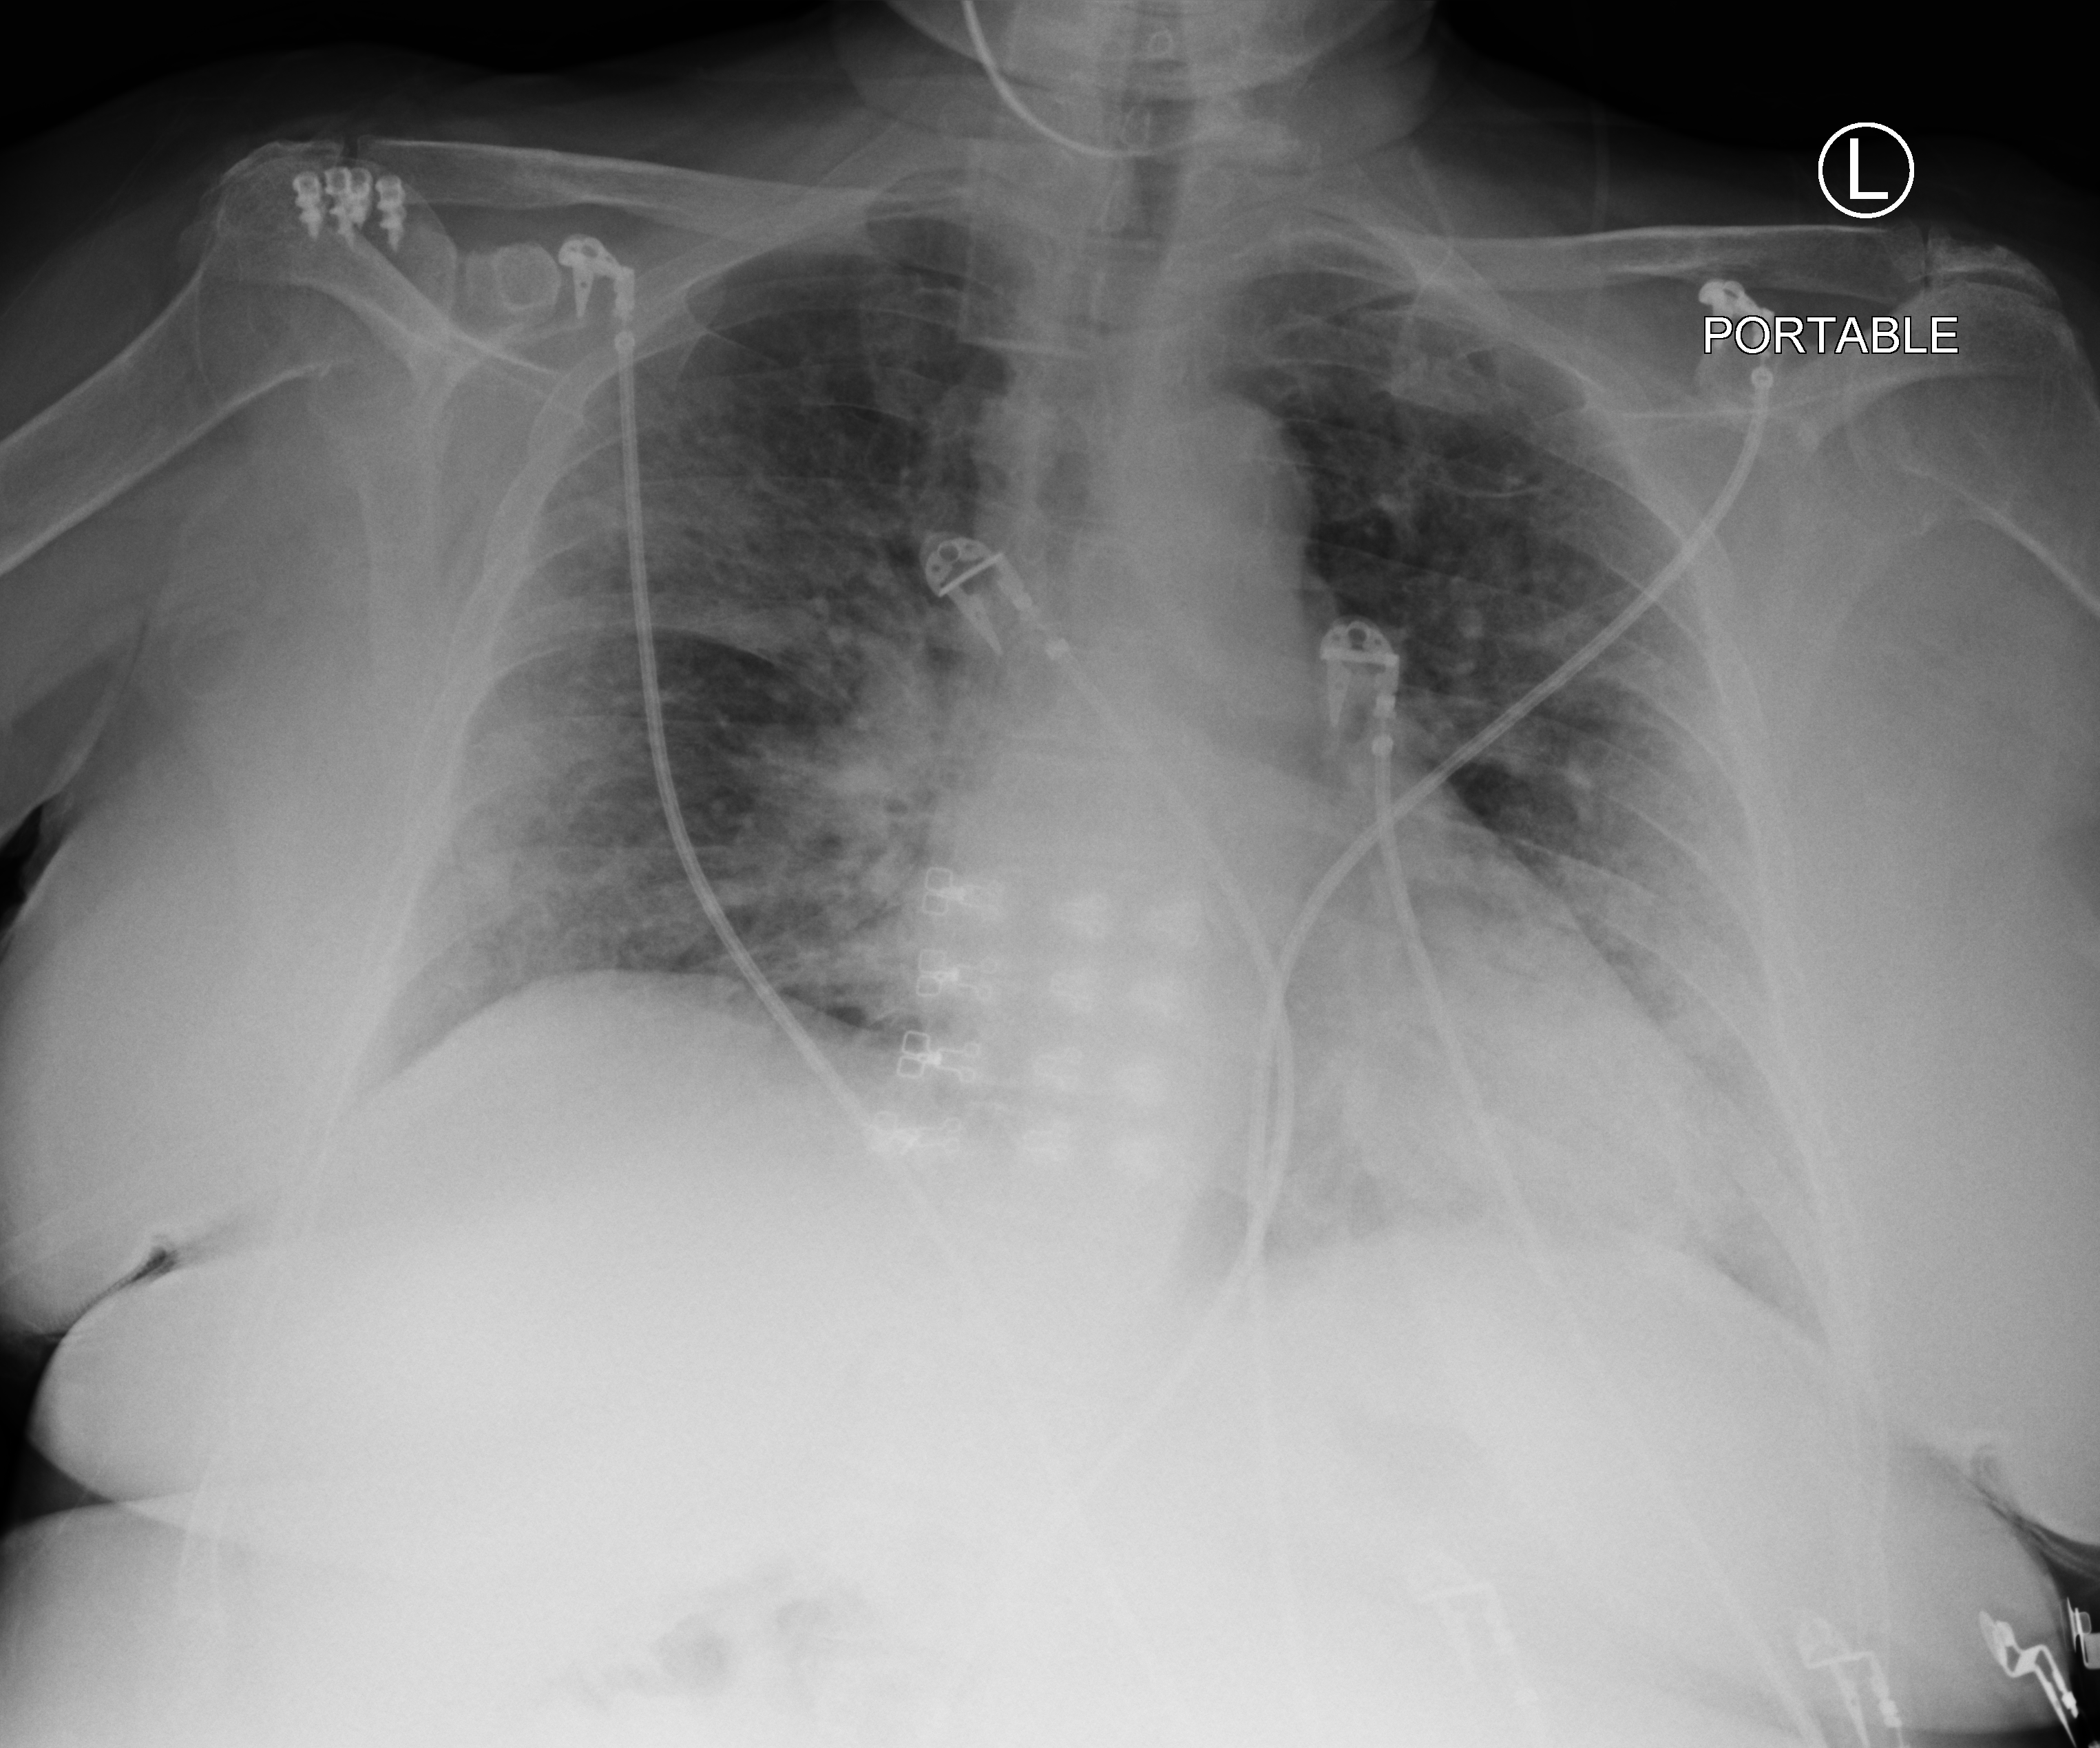
Portable chest radiograph. Patient hospitalised with COVID-19; female, aged 60–74 years.
Admission-level facts for this patient (not findings on this image; timing relative to this image not recorded): admitted to intensive care during this hospital stay: yes.